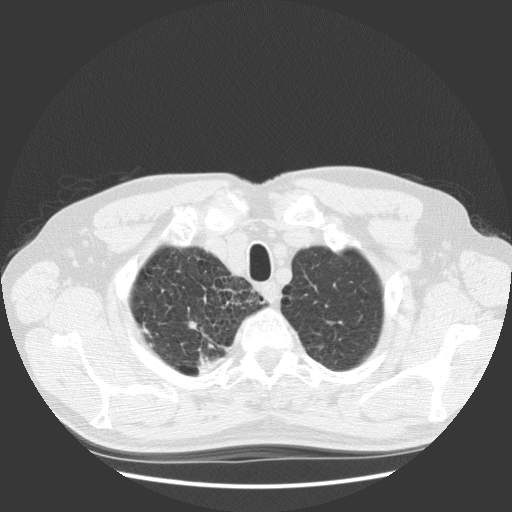
Low-dose screening chest CT, one axial slice. Position 113 of 131 along the scan axis. Lung window (W 1500 / L -600 HU). 2.5 mm slice thickness. 512 × 512 image matrix, field of view 369 × 369 mm.
Structures marked on this image (expert manual segmentation):
- lesion 1 (tumor, upper lobe of right lung): bounding box <197,345,230,375> (left, top, right, bottom; pixels)